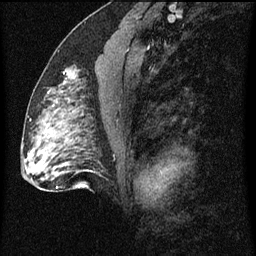
Breast MRI (dynamic contrast-enhanced), one sagittal slice. Position 35 of 60 along the scan axis. Dynamic contrast-enhanced series, image 2 of 3 at this slice position (ordered by acquisition). 1.5 T. TE 4.2 ms, TR 8 ms. 256 × 256 image matrix, field of view 180 × 180 mm. Female patient, age 51 years.
Outlined on this slice (semi-automatic segmentation, software-assisted and operator-edited):
- analysis volume of interest (the breast-tissue region the enhancement analysis was run in; not a lesion): bounding box (x1, y1, x2, y2) in pixels: (54, 50, 95, 103)
- tumour enhancement mask (voxels above the 70 % enhancement threshold inside the analysis volume of interest): (64, 72, 66, 75)